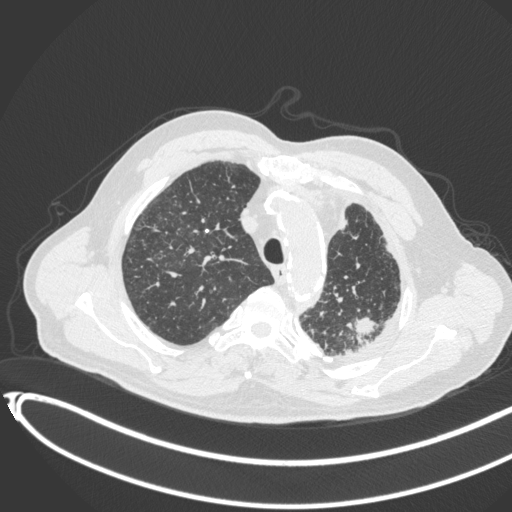
Chest CT, one axial slice. Reconstruction kernel B31f. Lung window (W 1500 / L -600 HU). 1 mm slice thickness. 512 × 512 image matrix. Patient: male, 78 years. Case-level facts recorded for this patient, not image findings: clinical TNM (as recorded): T1c N0 M1.
Outlined on this slice (bounding box drawn by a radiologist):
- lung tumour (recorded histology: adenocarcinoma): box from (x=347, y=311) to (x=382, y=343) px